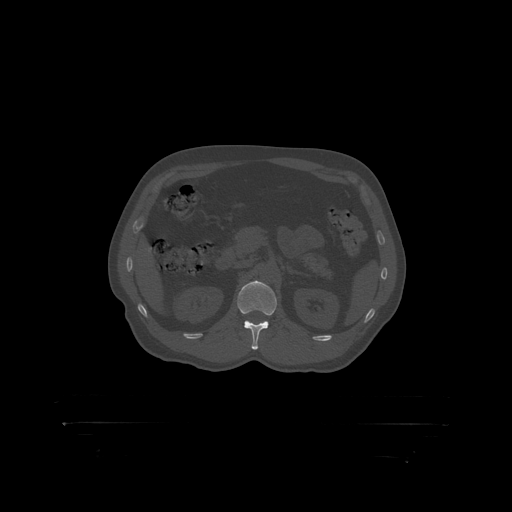
CT including the spine, one axial slice; slice 321 of 399 in the series (ordered by position); reconstruction kernel STANDARD; bone window (W 1800 / L 400 HU); 512 × 512 image matrix, field of view 650 × 650 mm. Male patient, age 46 years. Case-level facts recorded for this patient, not image findings: primary cancer: skin.
Annotated regions visible in this slice (semi-automatic segmentation, software-assisted and operator-edited):
- L1 vertebra: bounding box (x1, y1, x2, y2) in pixels: (237, 281, 278, 316)